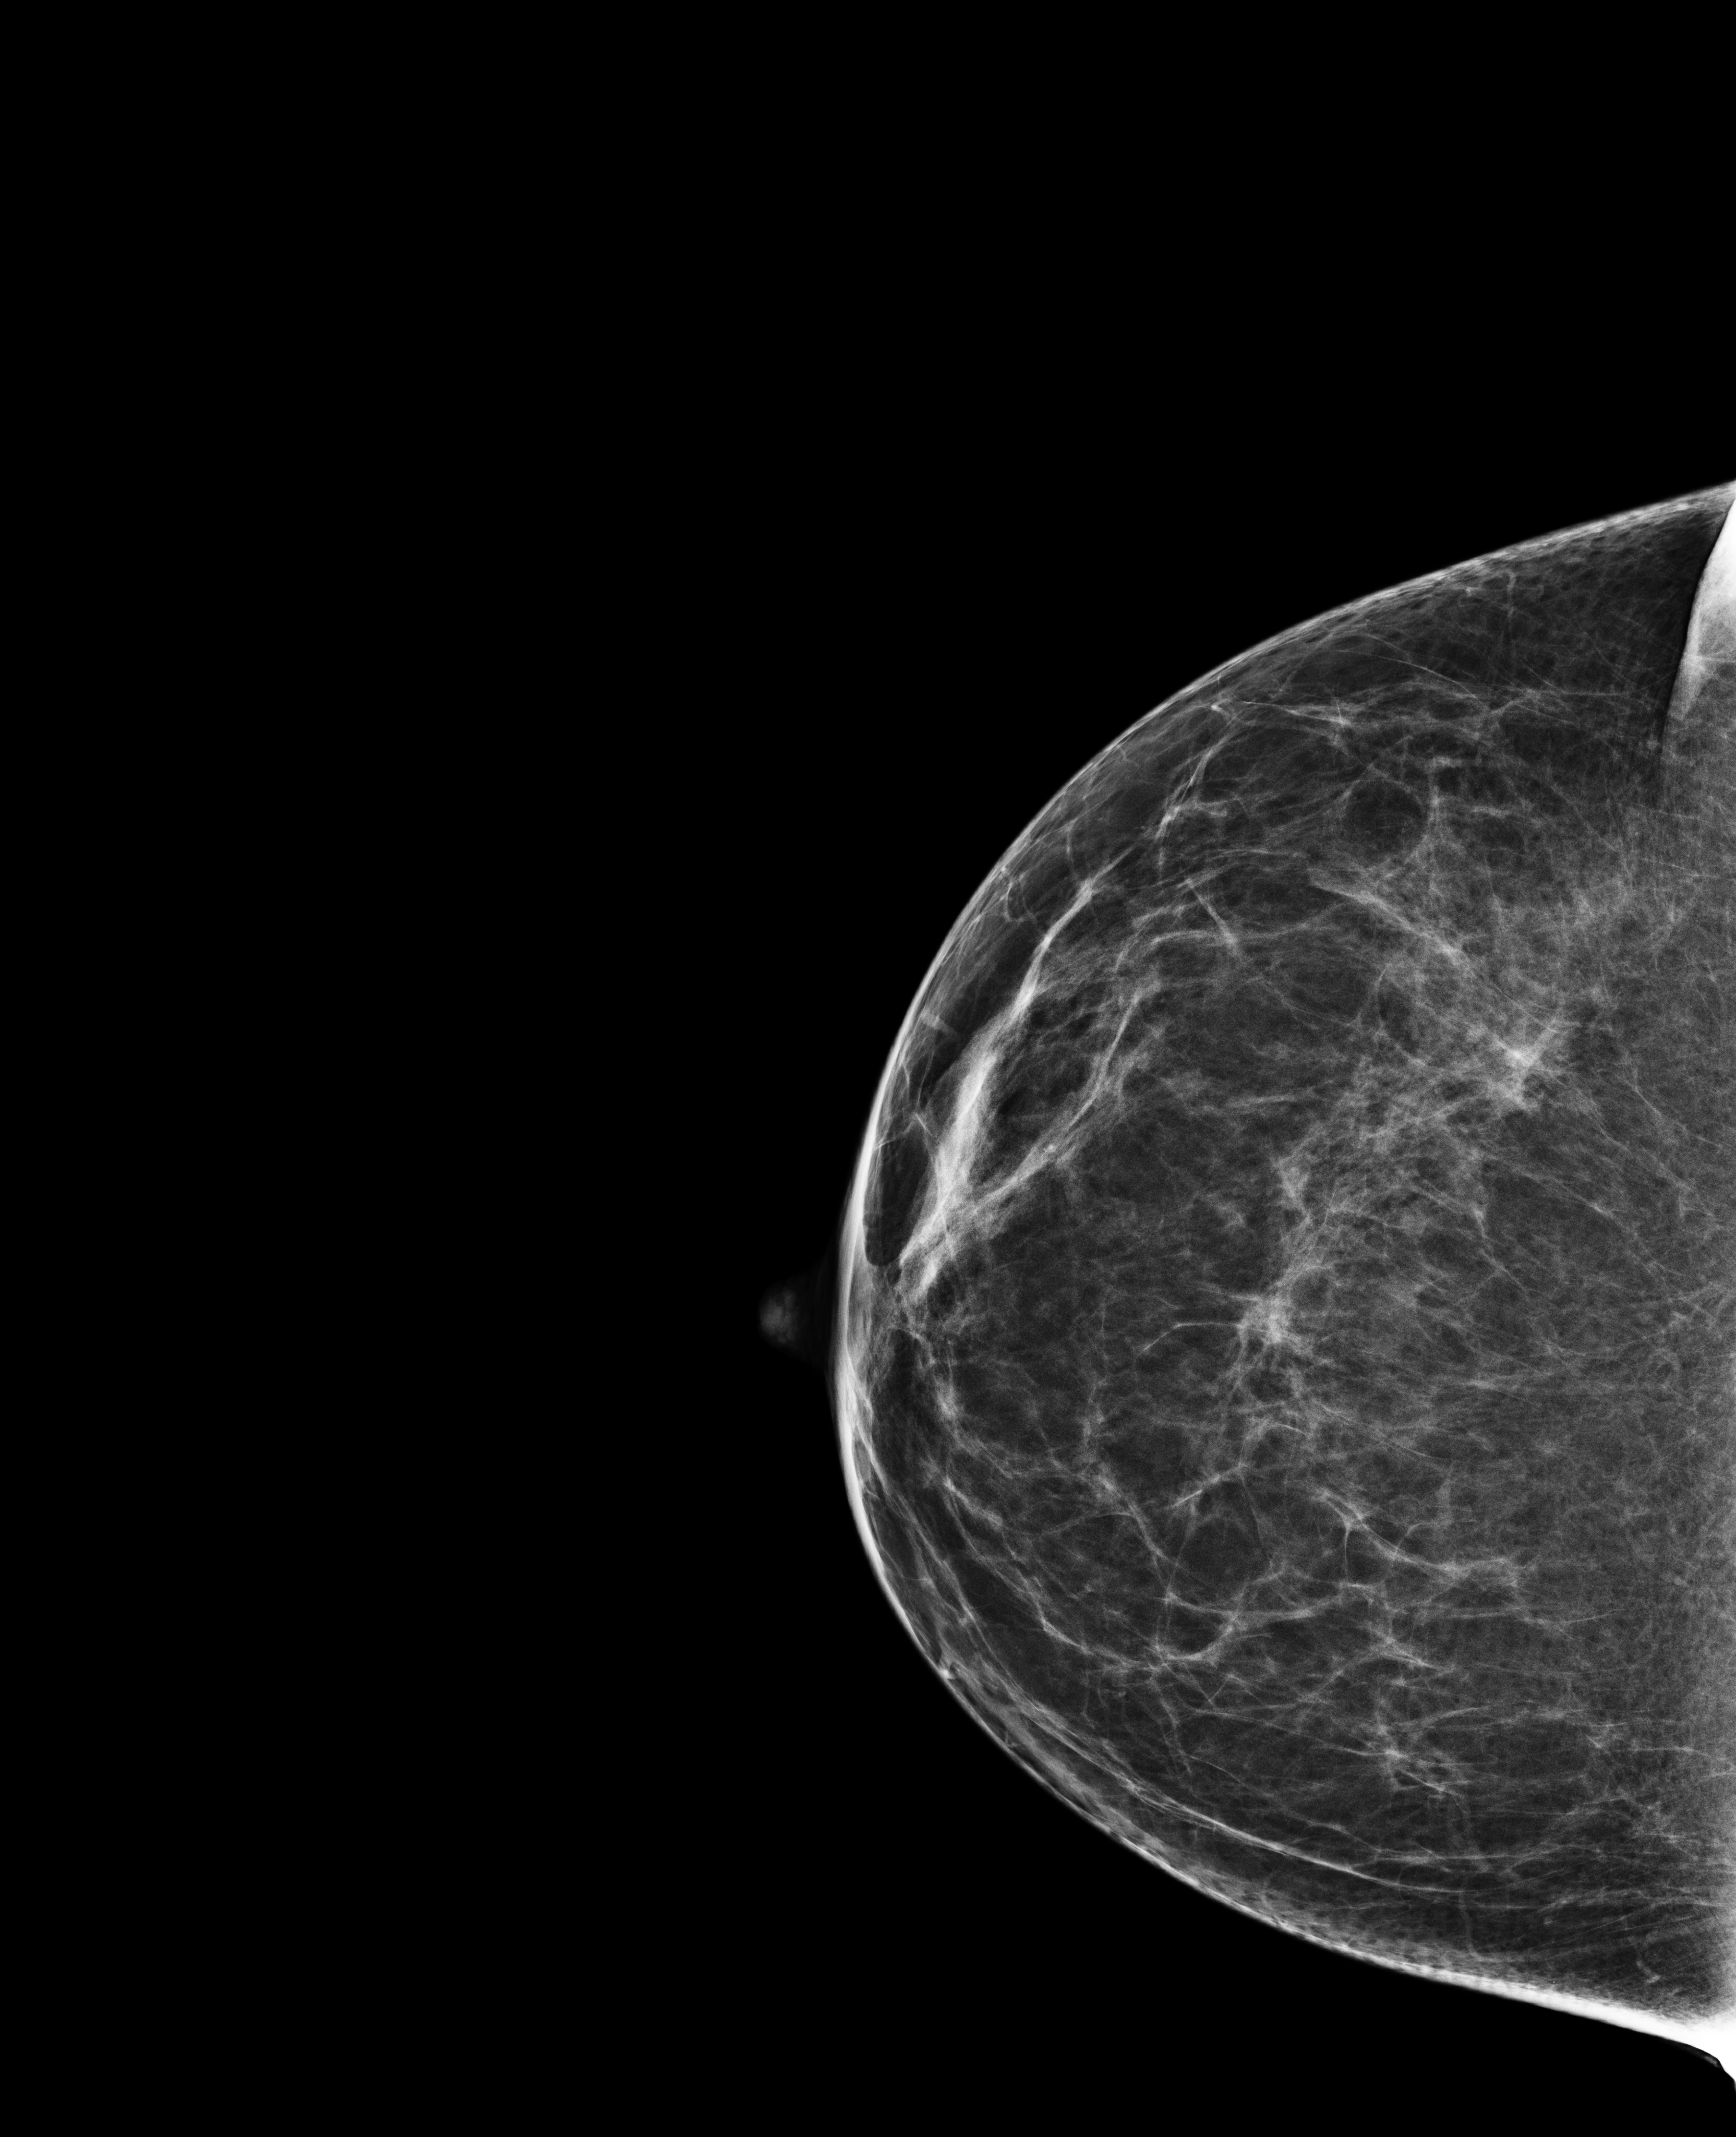
Digital mammogram (FFDM); right breast; CC view; annual screening mammography examination; compressed breast thickness 80 mm; system: Selenia Dimensions. Patient aged 41 years (female).
Breast density at the screening exam (both breasts): heterogeneously dense (BI-RADS density category c). Final BI-RADS category for the screening round (tomosynthesis exam, both breasts): category 1. Recall: no recall after this screen.